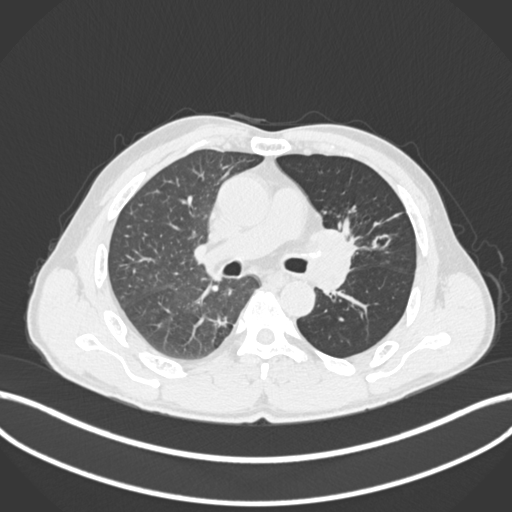
Chest CT, one axial slice. Slice 111 of 255 in the series (ordered by position). 120 kVp. Lung window (W 1500 / L -600 HU). 1 mm slice thickness. 512 × 512 image matrix, field of view 400 × 400 mm. Male patient, age 57 years. From the clinical record (not read from this slice): clinical TNM (as recorded): T2b N0 M0.
Outlined on this slice (rectangle marked by the reading radiologist):
- lung tumour (recorded histology: squamous cell carcinoma): bounding box [x1, y1, x2, y2] px = [305, 218, 360, 258]